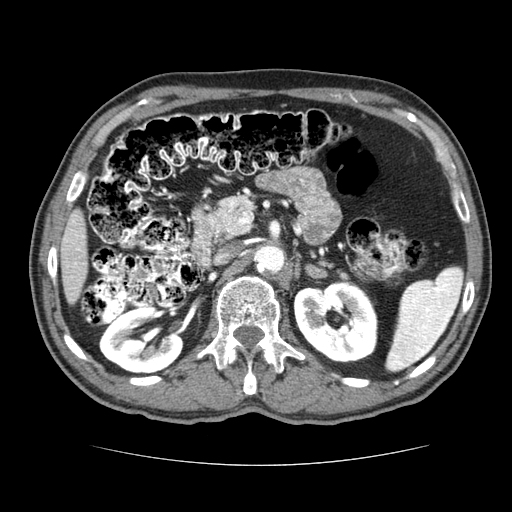
Contrast-enhanced abdominal CT (liver protocol), one axial slice; reconstruction kernel STANDARD; 120 kVp; soft-tissue window (W 400 / L 40 HU); 2.5 mm slice thickness; 512 × 512 image matrix, field of view 360 × 360 mm. Case-level facts recorded for this patient, not image findings: diagnosis: hepatocellular carcinoma (patient treated with transarterial chemoembolisation; whether this scan precedes or follows treatment is not stated here); TNM stage (as recorded): Stage-I; Child-Pugh class: A; tumour nodularity: uninodular.
Annotated regions visible in this slice (semi-automatic segmentation, software-assisted and operator-edited):
- liver parenchyma outside the tumour (the mass and vessels are separate outlines, so this box may not span the whole liver): bounding box [x1, y1, x2, y2] px = [60, 208, 86, 304]
- liver vessels: [65, 220, 84, 265]